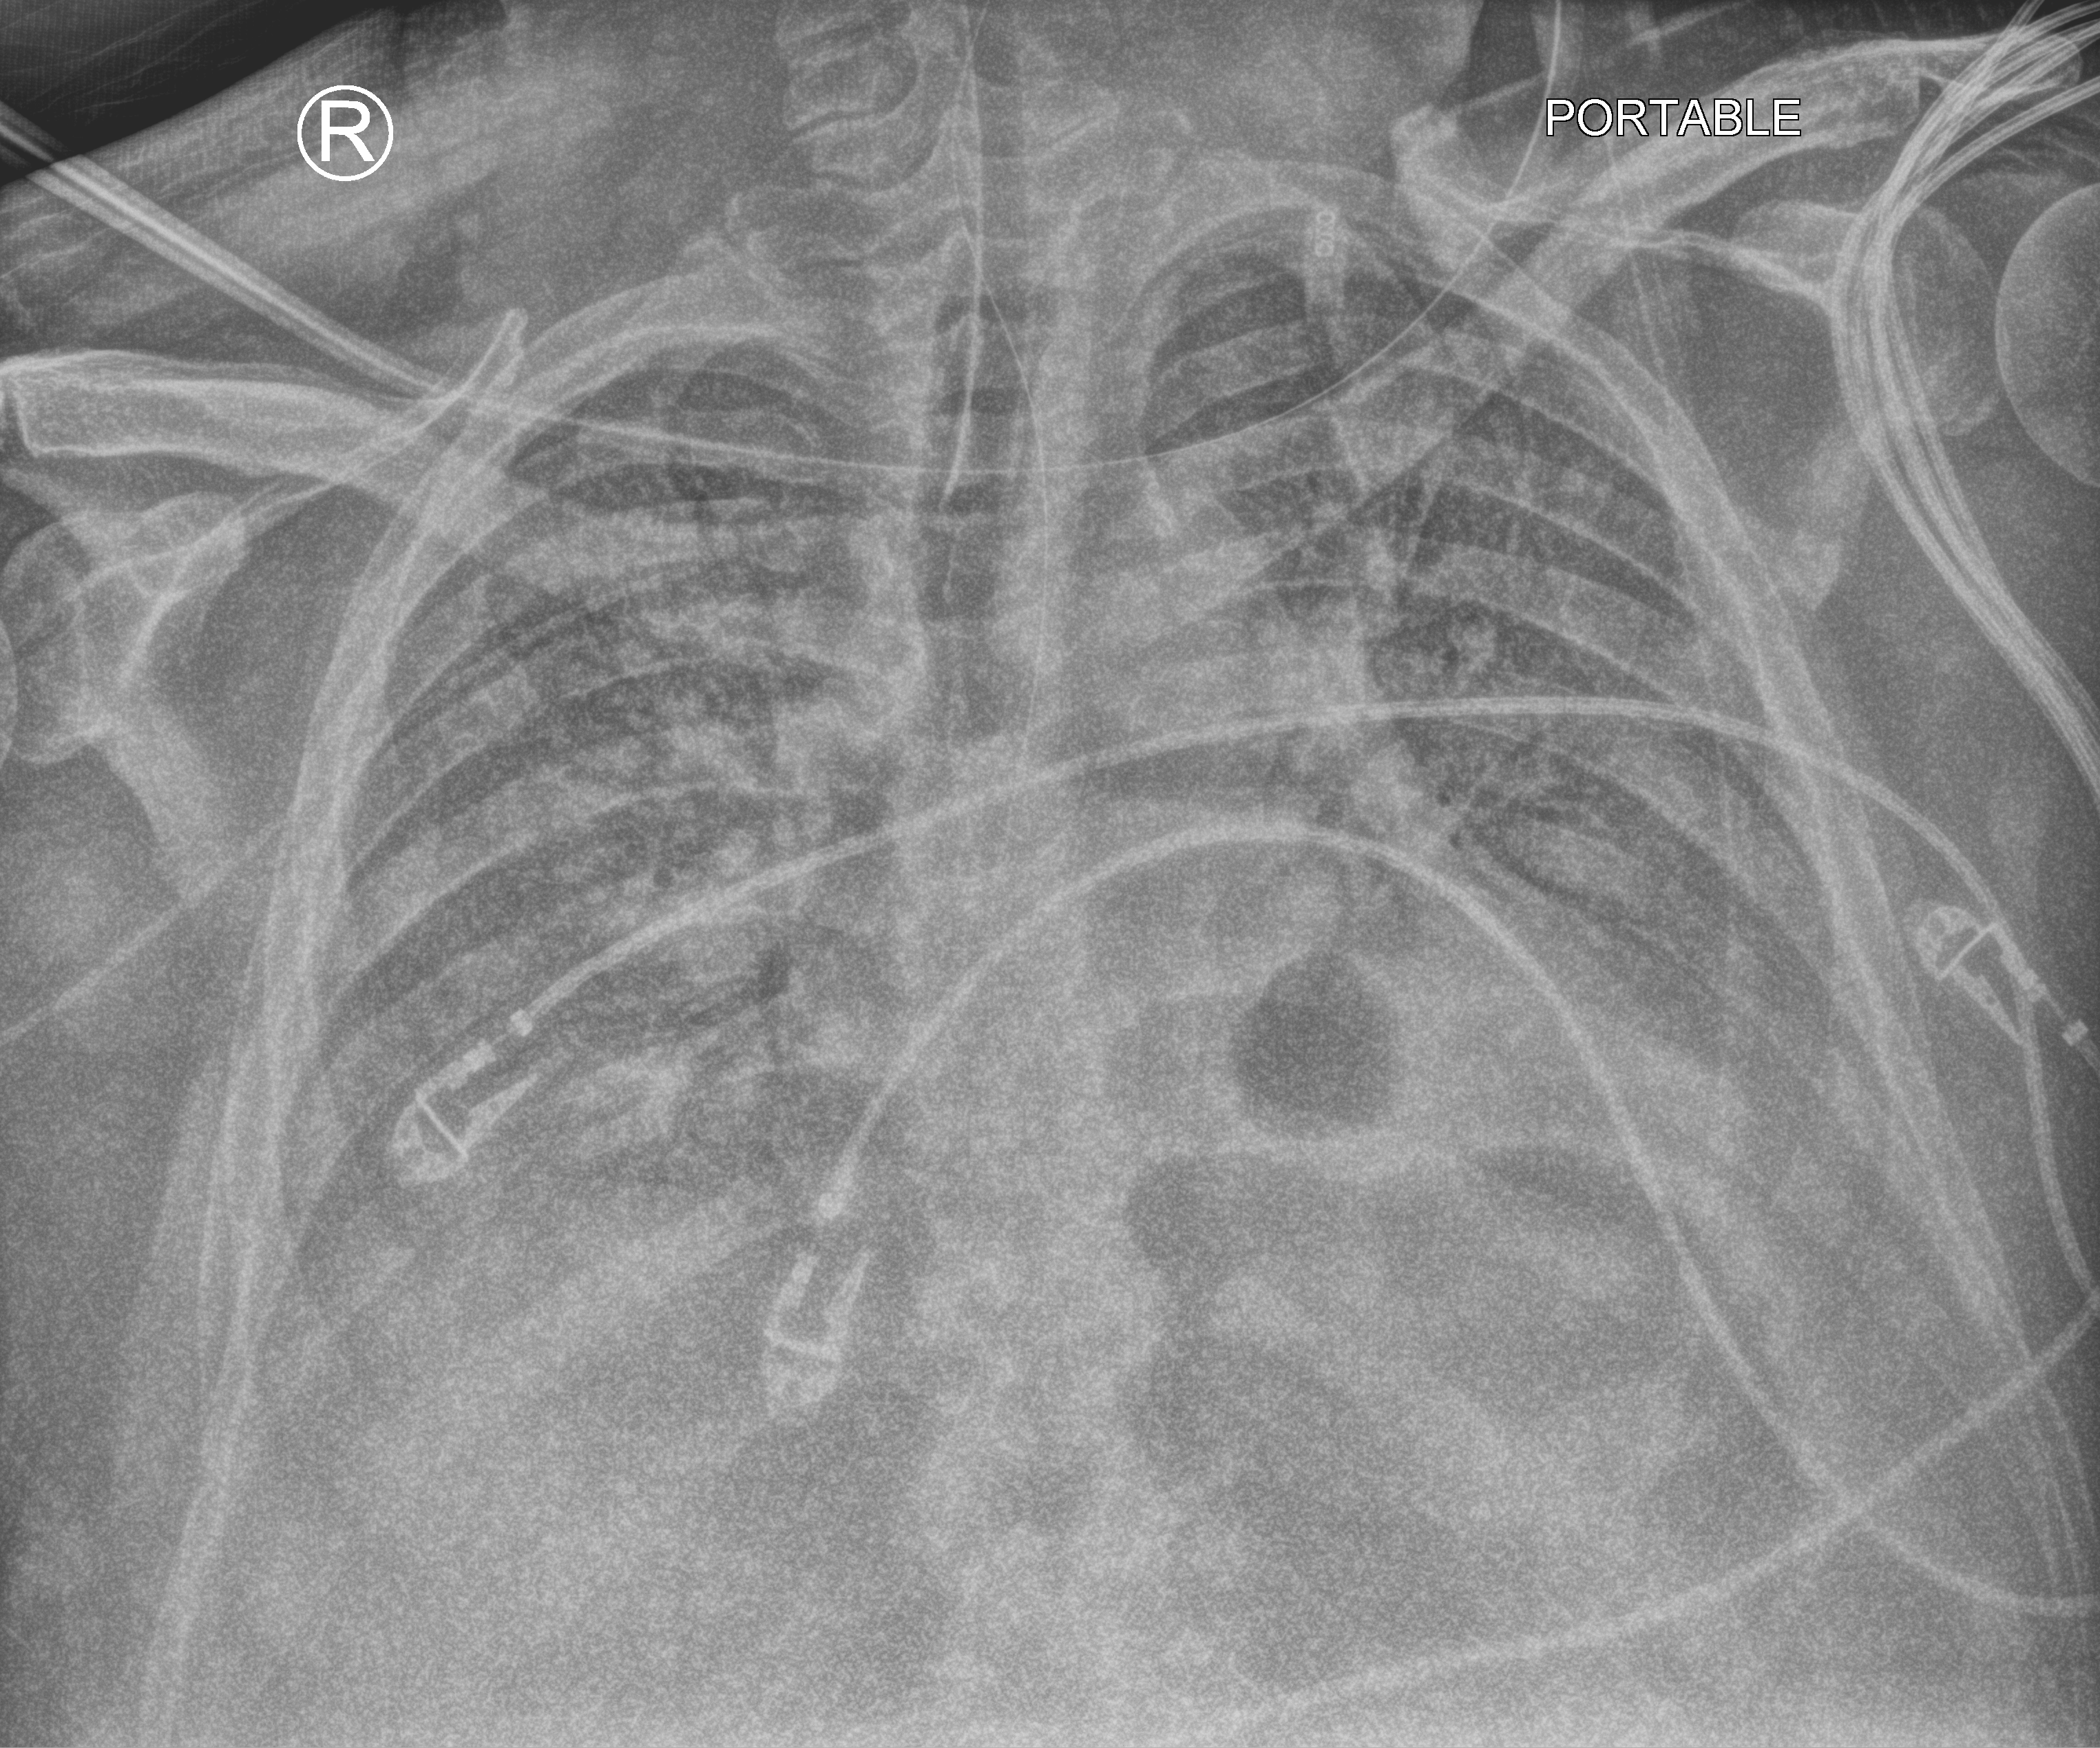
Chest X-ray (portable), anteroposterior (AP) projection. Adult patient hospitalised with COVID-19, age 18–59 years.
From the hospital-stay record, not from the radiograph (when in the stay this image was taken is not recorded): length of hospital stay: 26 days; admitted to intensive care during this hospital stay: yes.